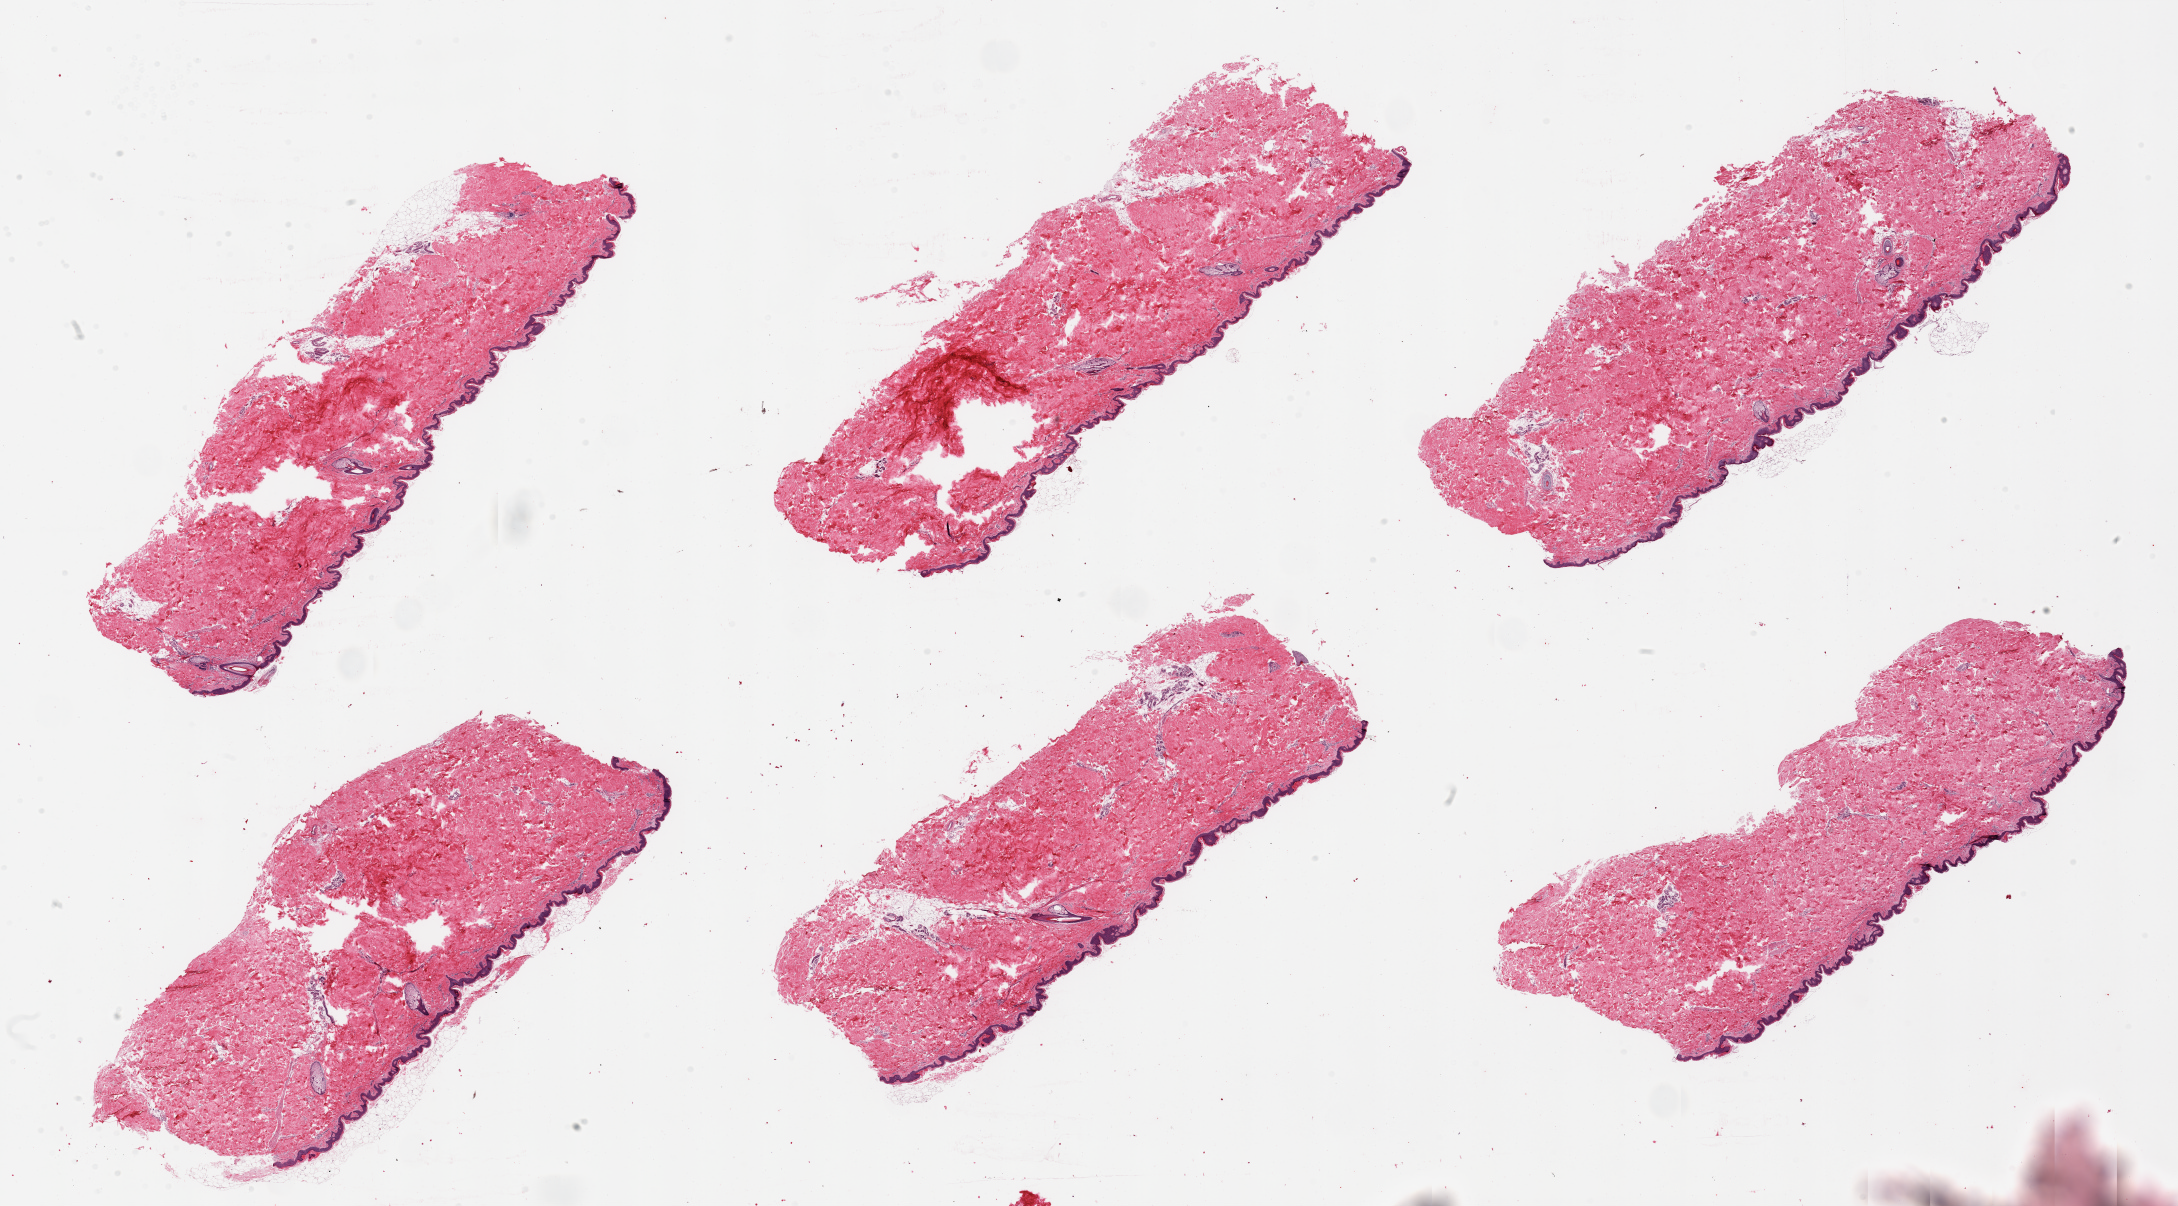
Whole-slide image, haematoxylin and eosin stain, shown as a low-resolution overview of the whole scanned area (about 34.5 x 19.1 mm); PAXgene-fixed paraffin-embedded (PFPE) section; target tissue: skin of lower leg; tissue donor sample. Donor sex: male.
* pathologist's review note for this sample: 6 pieces; predominantly well trimmed with minimal internal/external fat, epidermis measures 40 microns